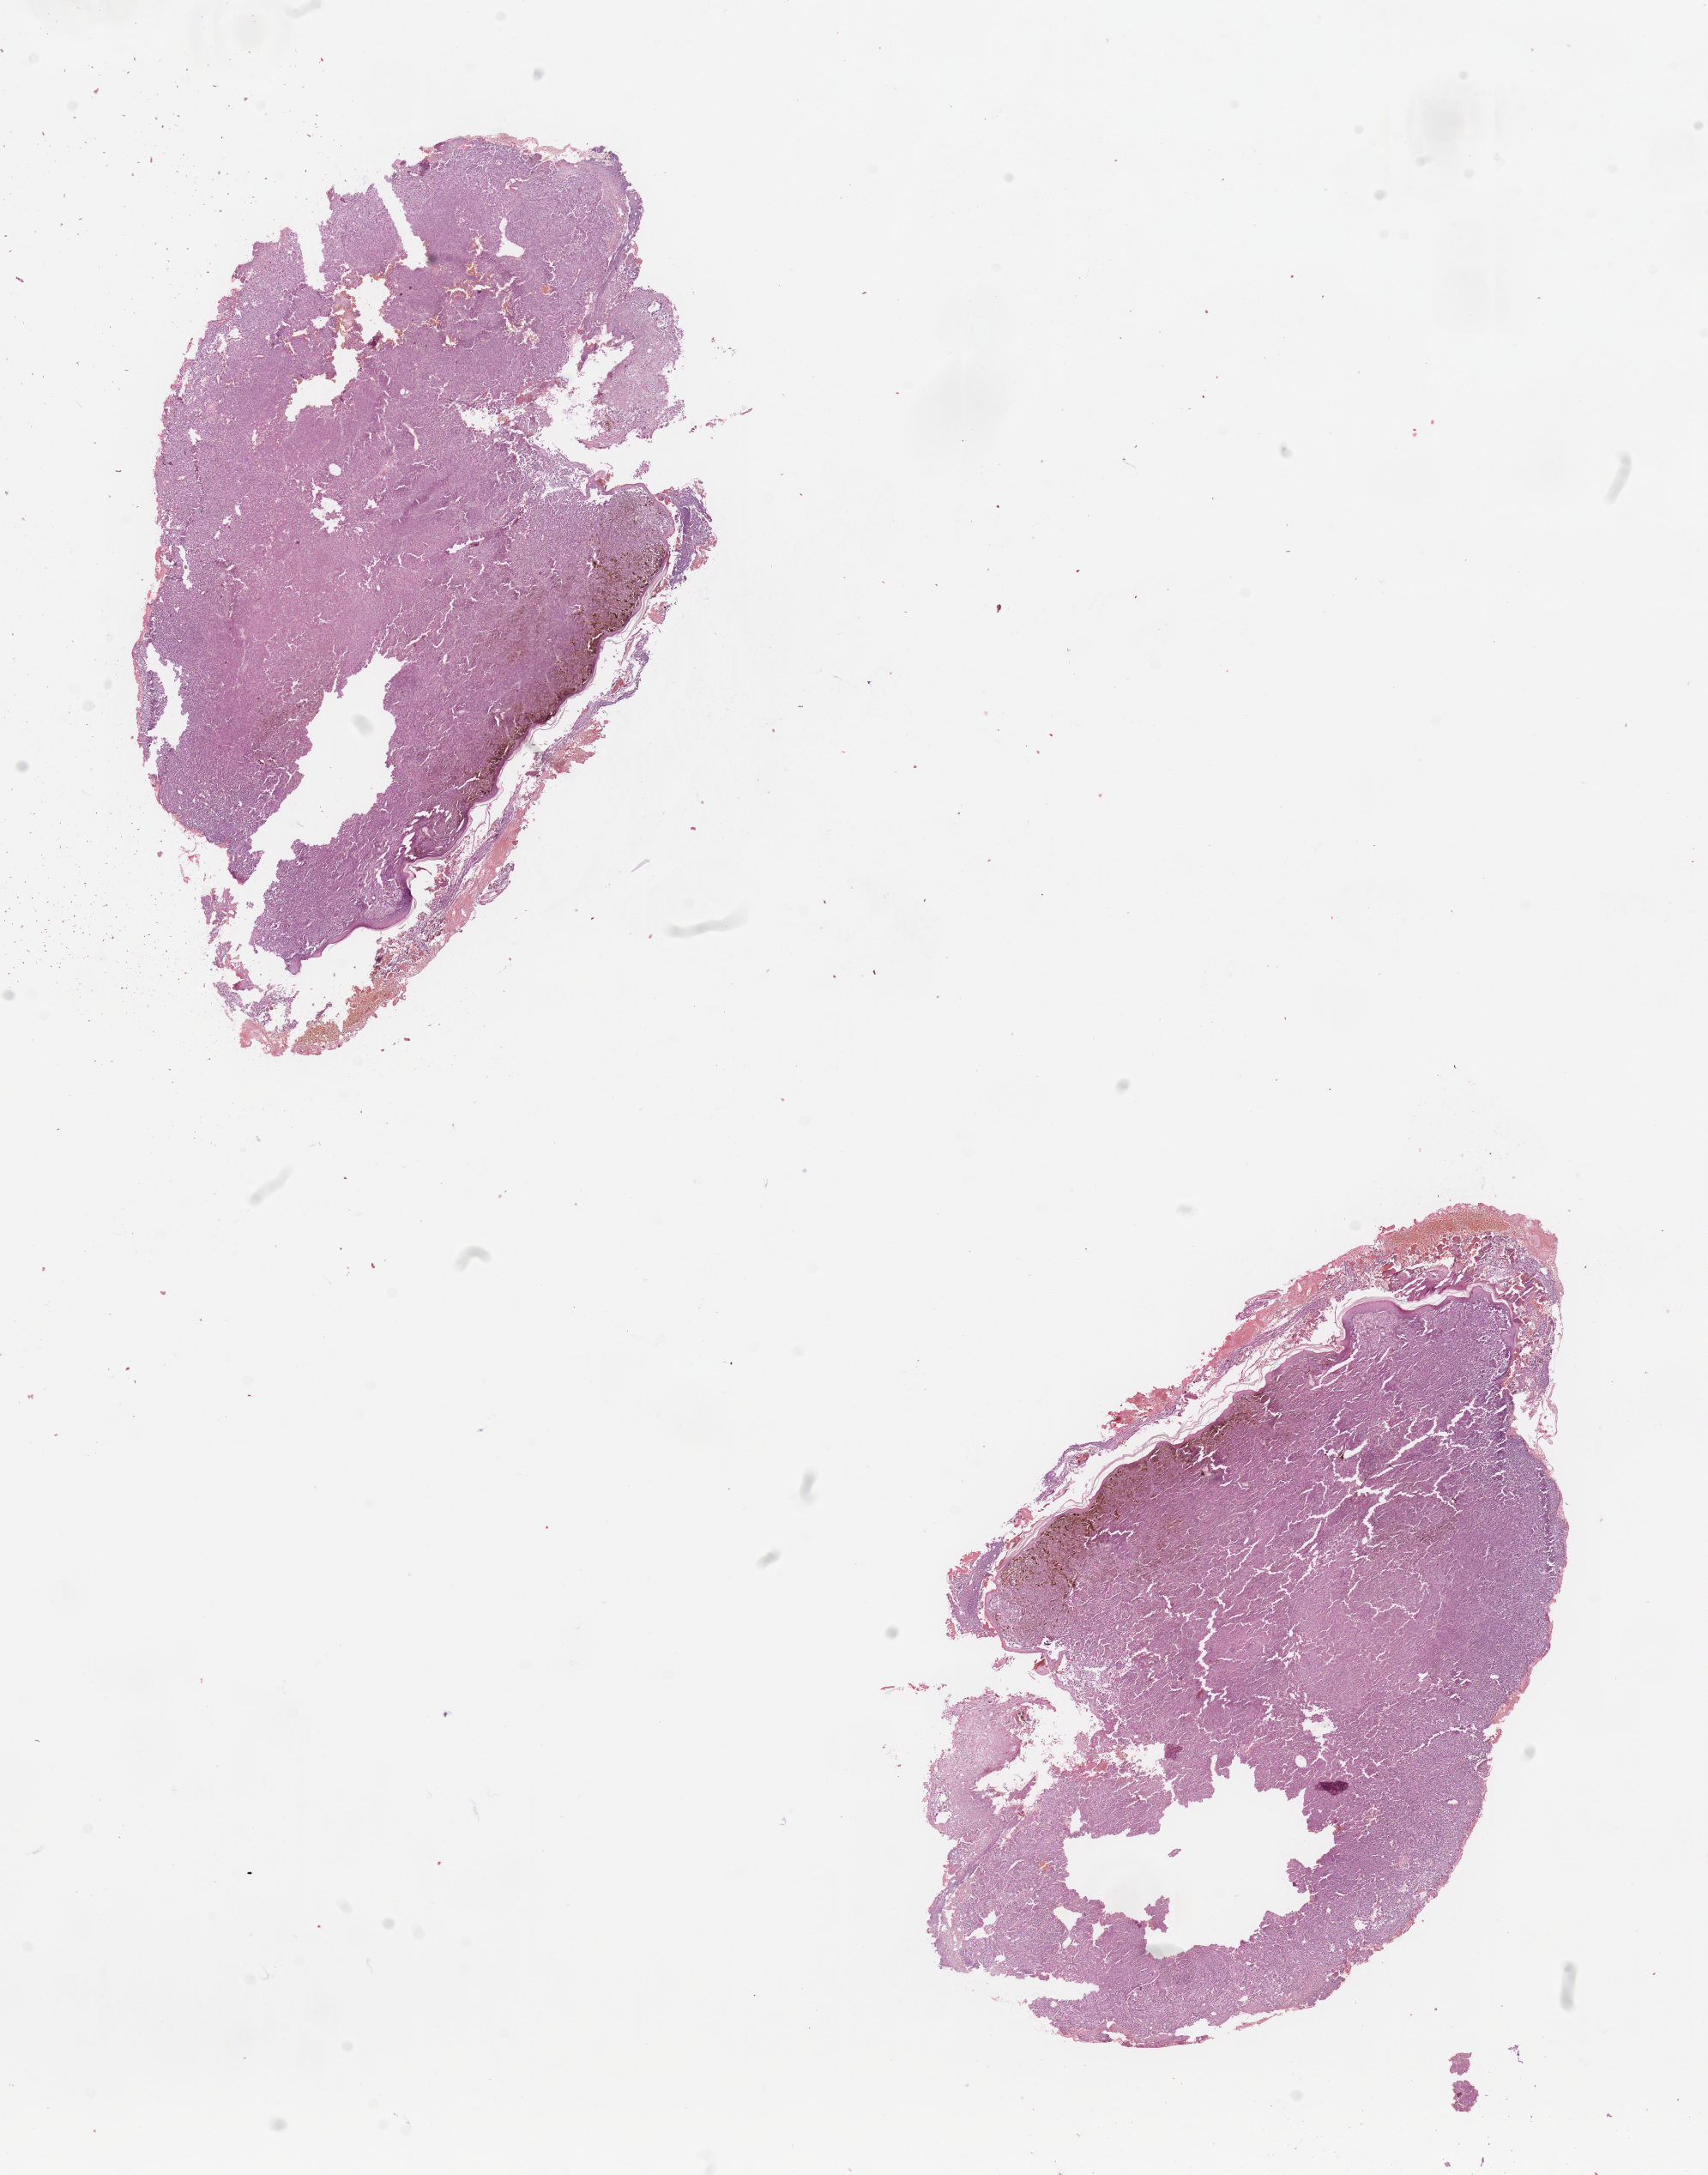
Digitized Hematoxylin and eosin (H&E) stained tissue section (whole slide) — low-resolution overview of the scanned area, about 15.8 x 20.1 mm (from a 20x scan). Tumour tissue sample, sampled site: trunk. Patient: female, age 86 years. Slide review estimates, as recorded: tumour nuclei 95%, necrosis 0%.
Primary tumour site (as recorded): trunk. Diagnosis: Malignant melanoma, NOS. AJCC pathologic stage: IIC.